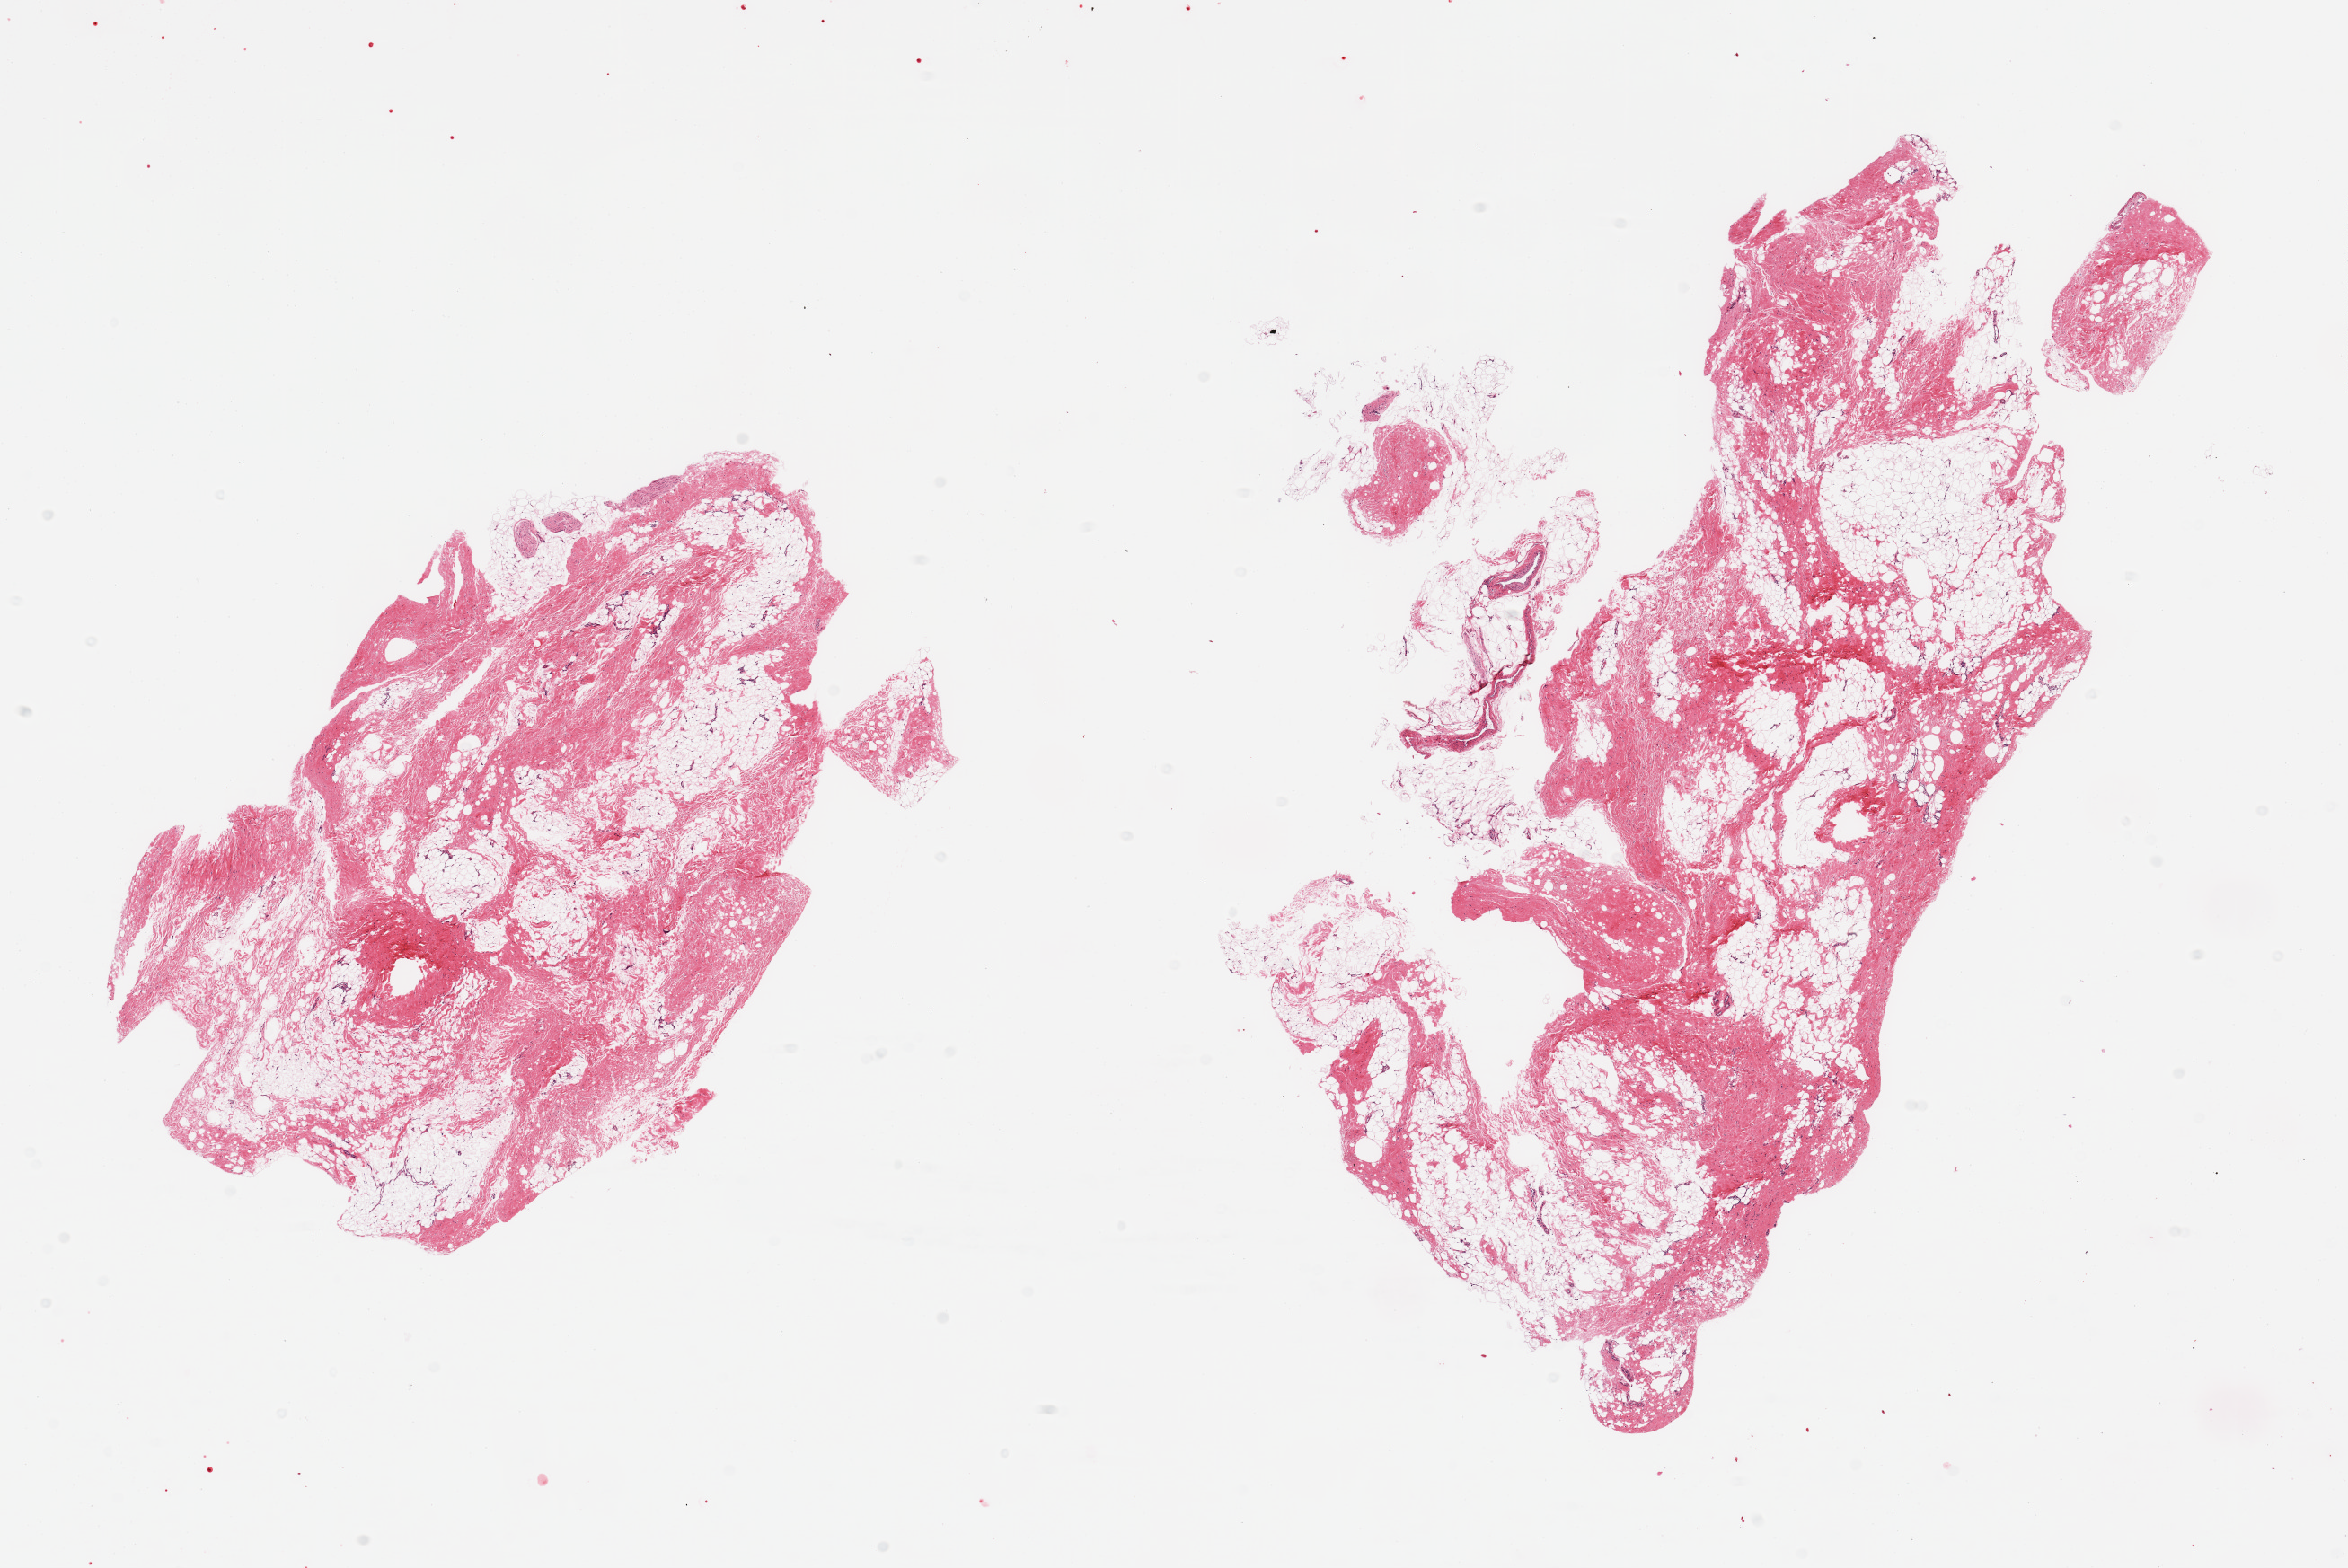
Whole-slide image, hematoxylin and eosin (H&E) stain — whole scanned area (about 20.7 x 13.8 mm, from a 20x scan) shown as a low-resolution overview. PAXgene-fixed, paraffin-embedded tissue. Target tissue: breast. Tissue donor sample. Donor sex: male.
Review note (as recorded): 2 pieces, fibroadipose elements only.